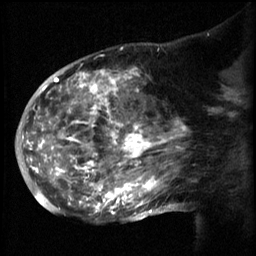
Breast MRI (dynamic contrast-enhanced), one sagittal slice. 3 images stored at this slice position (order not interpretable as contrast timing). 1.5 T. TE 4.2 ms, TR 8.2 ms. 256 × 256 image matrix. Patient: female, 50 years.
Outlined on this slice (semi-automatically segmented with operator editing):
- analysis volume of interest (the breast-tissue region the enhancement analysis was run in; not a lesion): bounding box (x1, y1, x2, y2) in pixels: (50, 64, 169, 217)
- tumour enhancement mask (voxels above the 70 % enhancement threshold inside the analysis volume of interest): (50, 66, 169, 215)